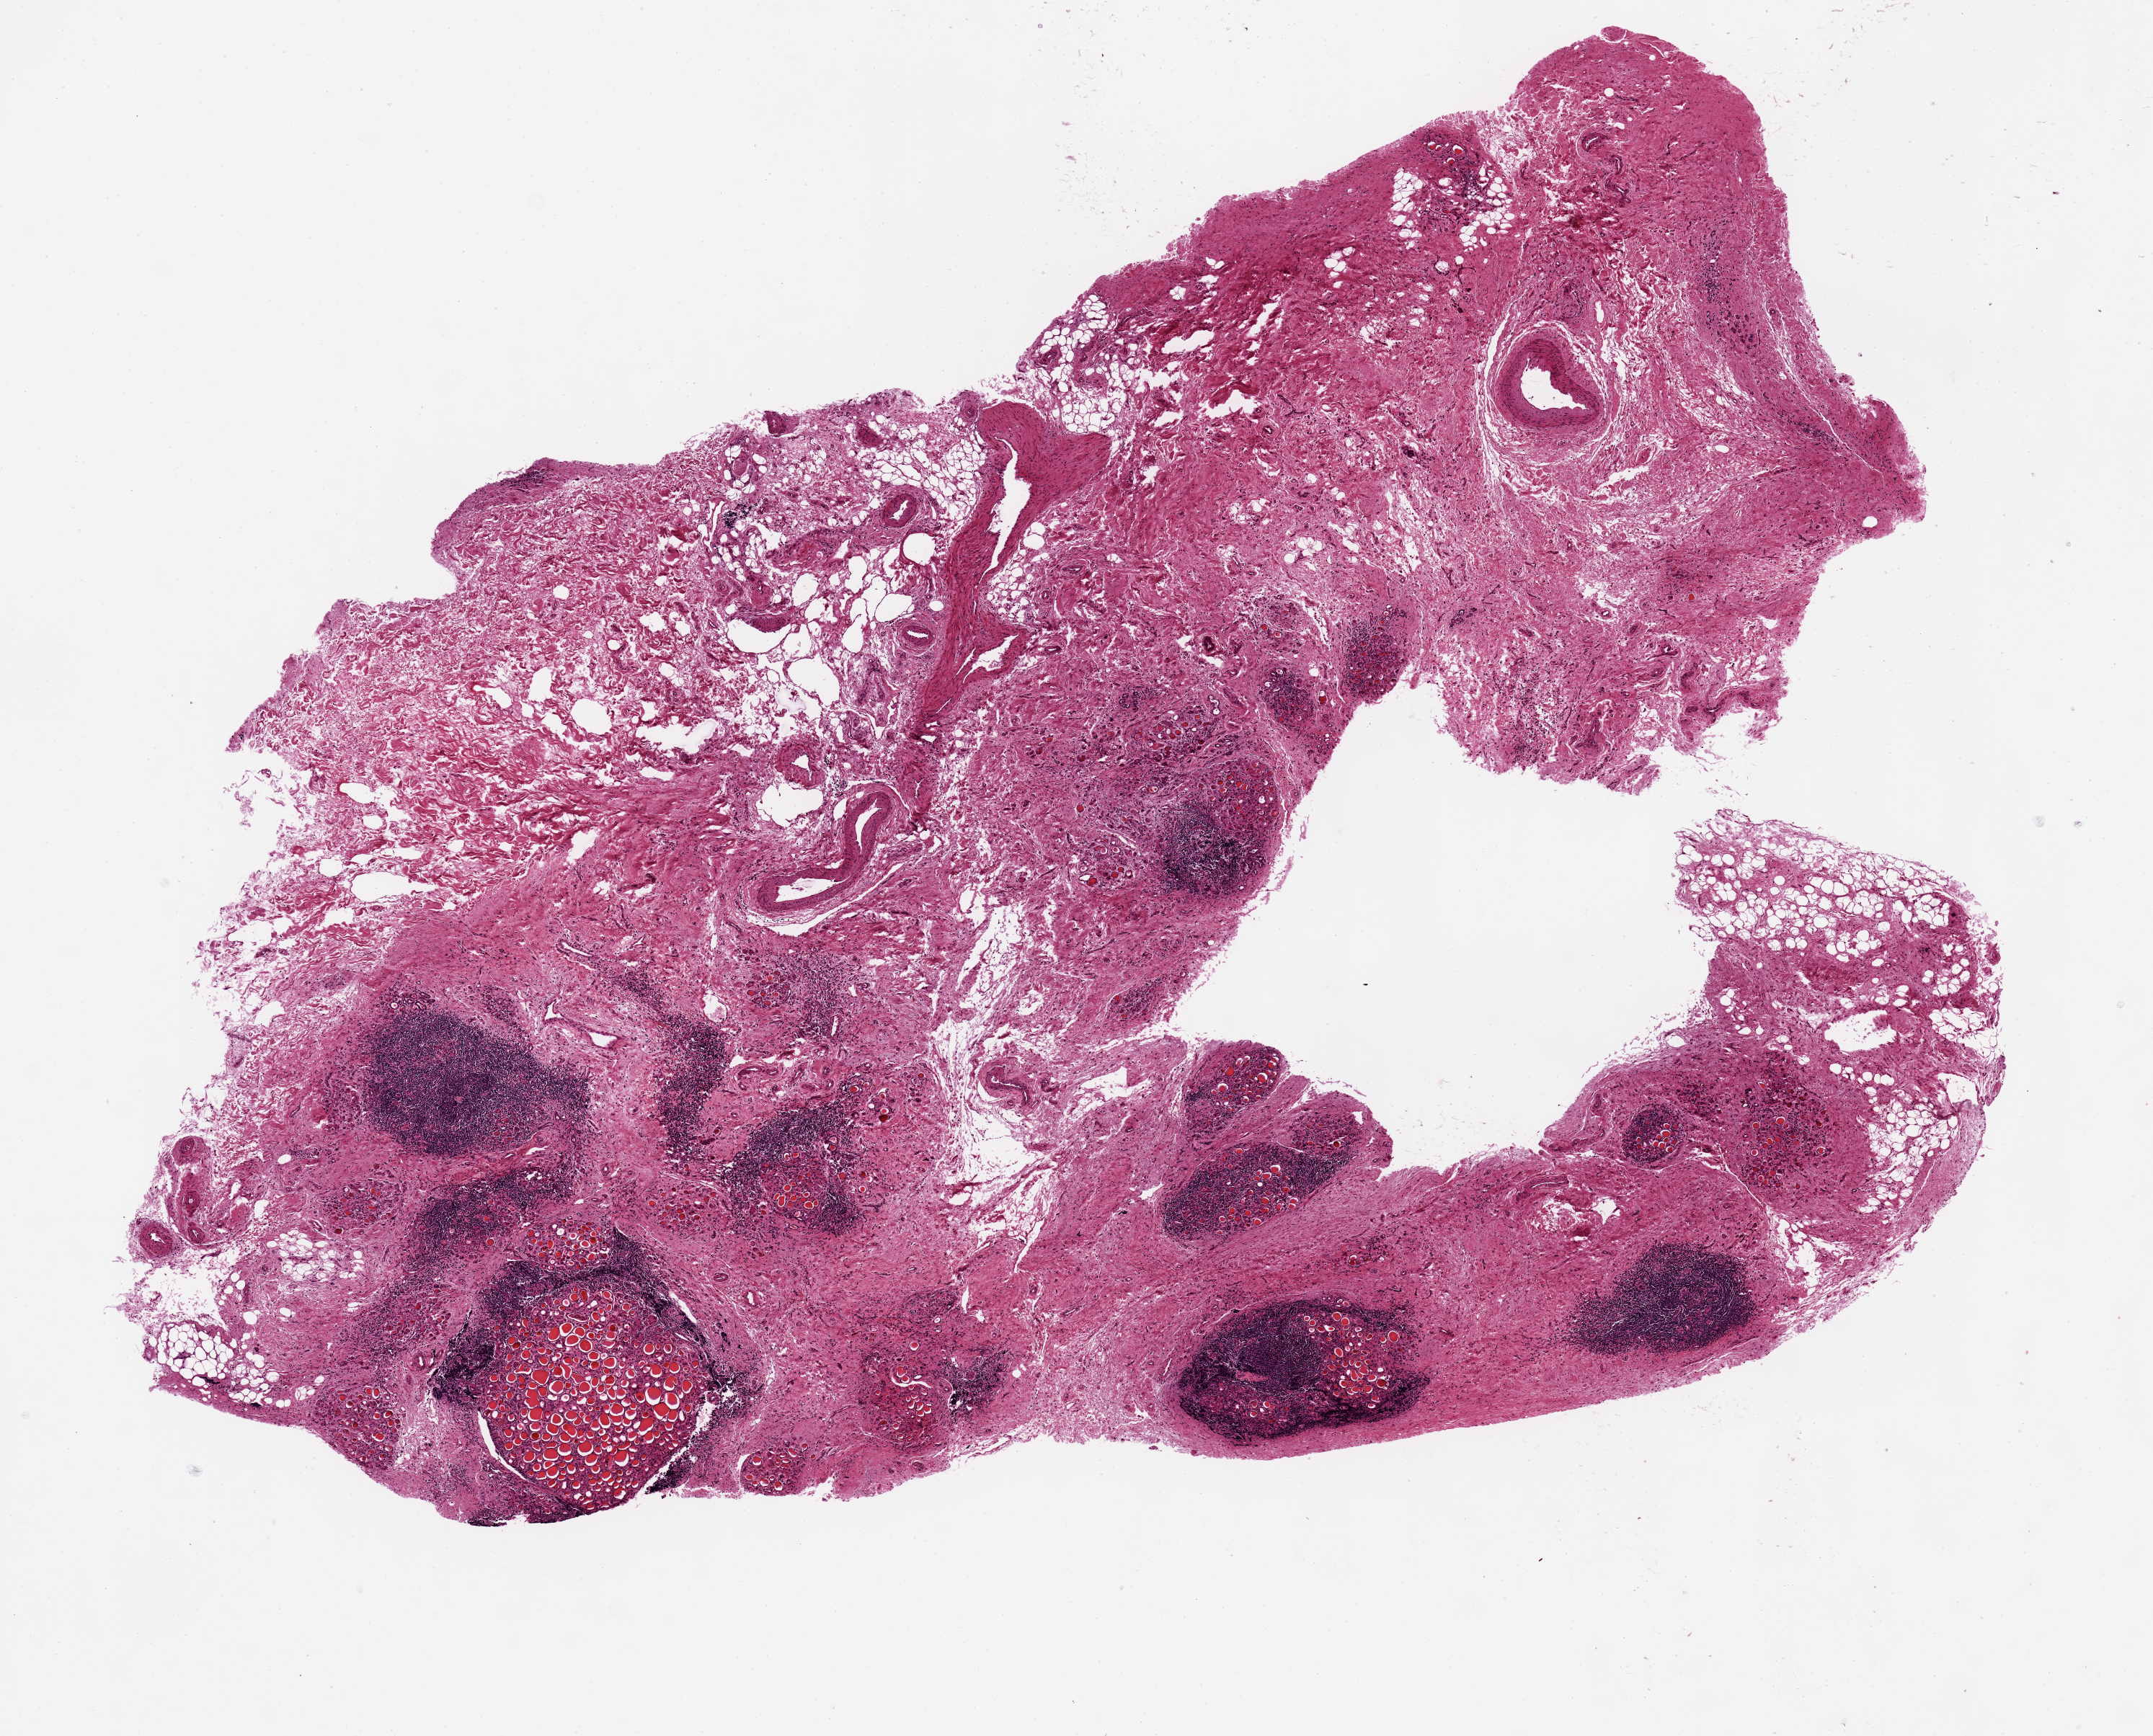
Whole-slide image, haematoxylin and eosin stain, low-resolution overview of the scanned area, about 11.8 x 9.5 mm. PAXgene-fixed paraffin-embedded (PFPE) section. Target tissue: thyroid. Tissue donor sample.
Pathologist's review note for this sample: Chronic inflammation, atrophy, fibrosis (severe) consistent with Hashimoto???s thyroiditis.